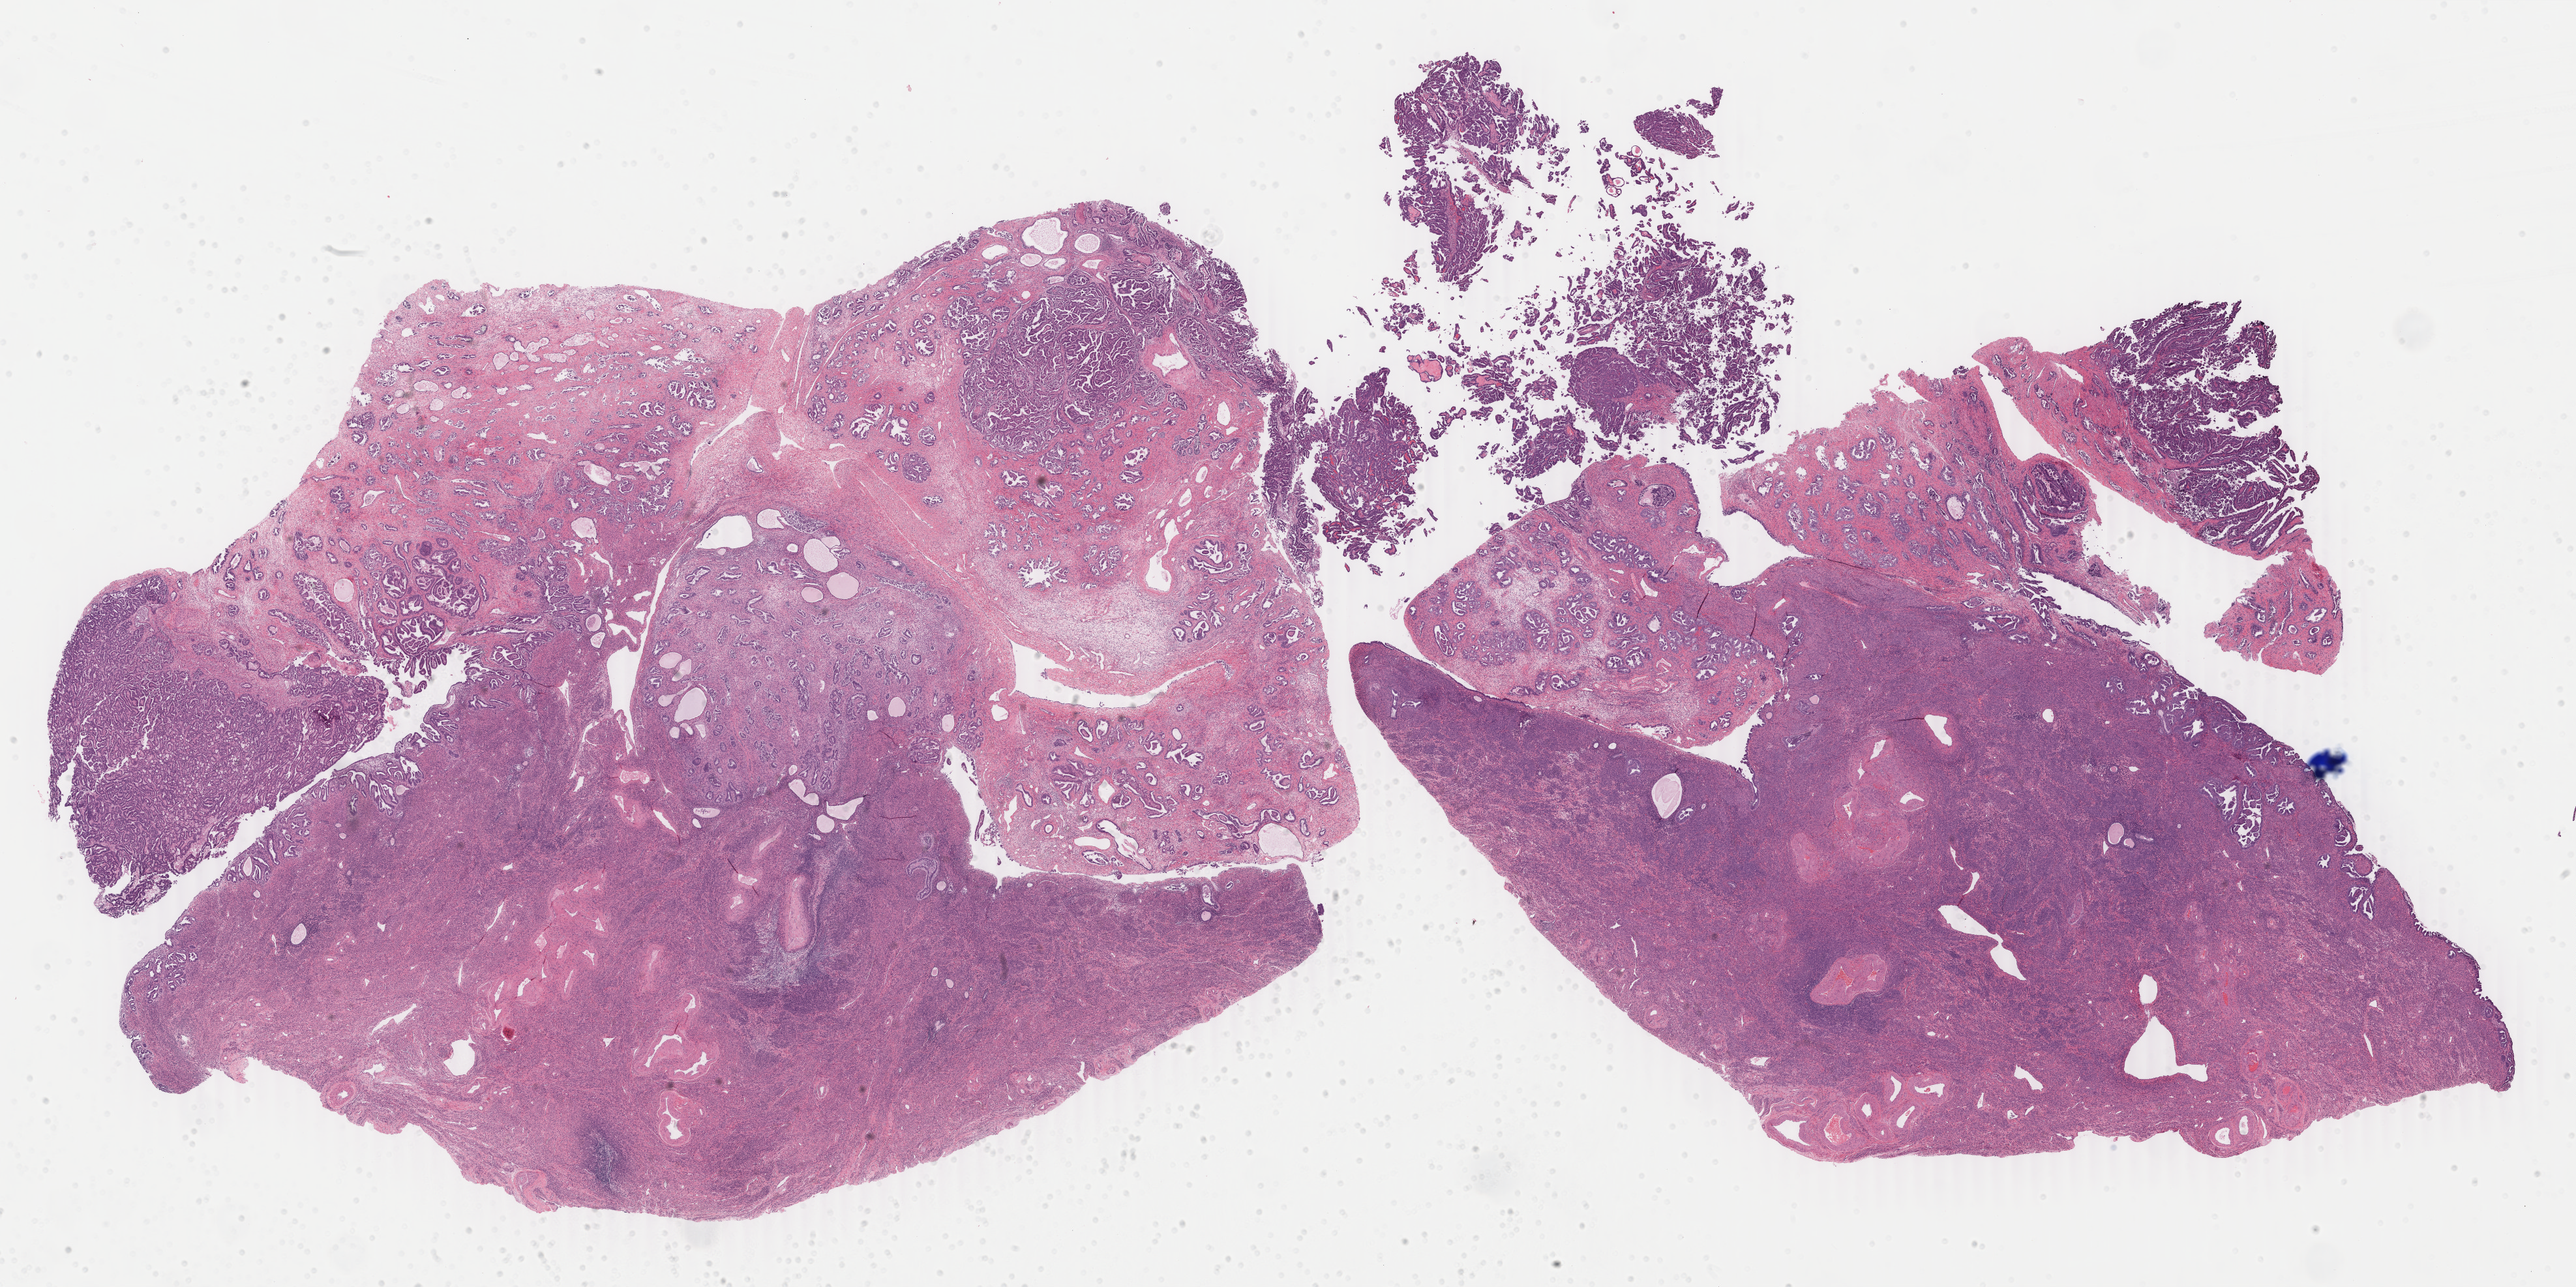
Digitized H&E-stained tissue section (whole slide) — low-resolution overview of the scanned area, about 31.4 x 15.7 mm (from a 40x scan), formalin-fixed paraffin-embedded (FFPE) diagnostic section, uterus, primary tumour sample. Female patient; age at initial diagnosis 80 years. Histologic grade: G3 (poorly differentiated).
- histologic diagnosis: Endometrioid adenocarcinoma, NOS (endometrium)
- FIGO stage: IB